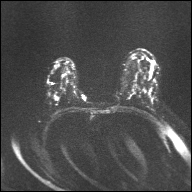
Breast MRI, one axial slice; position 23 of 32 along the scan axis; diffusion-weighted series; image 2 of 4 stored at this slice position (different b-values; order by instance number); 1.5 T; 4 mm slice thickness; 192 × 192 image matrix. Female patient.
Annotated regions visible in this slice (outlined manually by an expert reader):
- tumour on diffusion-weighted imaging: bounding box <54,96,58,100> (left, top, right, bottom; pixels)